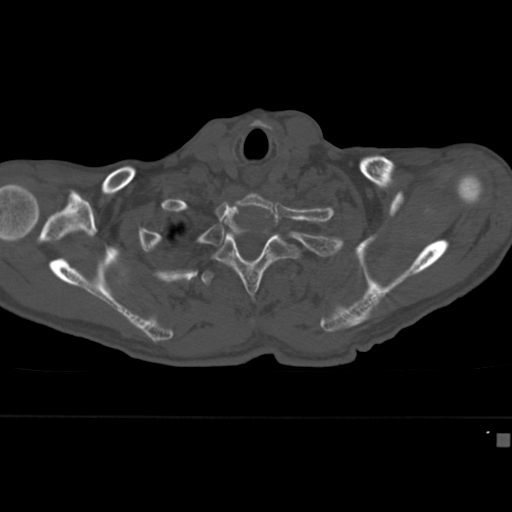
CT including the spine, one axial slice. Slice 345 of 430 in the series (ordered by position). Reconstruction kernel Br40s. Bone window (W 1800 / L 400 HU). 512 × 512 image matrix, field of view 337 × 337 mm. Patient: male, 64 years. From the clinical record (not read from this slice): primary cancer: uterus; vertebrae with lytic lesions (as recorded): T1, T4, T5, T7, L5.
Outlined on this slice (semi-automatic segmentation, software-assisted and operator-edited):
- T2 vertebra: bounding box (x1, y1, x2, y2) in pixels: (212, 232, 301, 299)
- T3 vertebra: (201, 261, 295, 325)